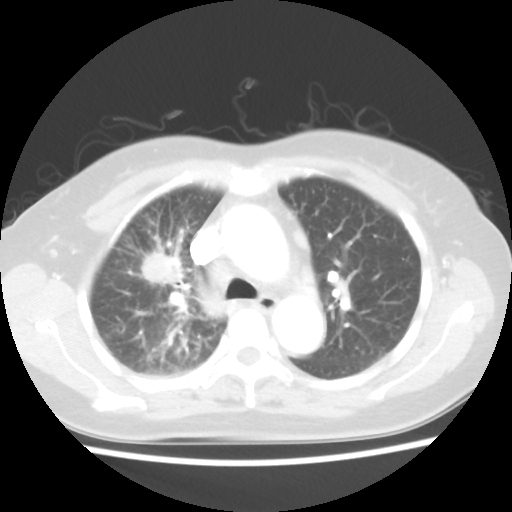
Chest CT, one axial slice; slice 31 of 48 in the series (ordered by position); 100 kVp; lung window (W 1500 / L -600 HU); 512 × 512 image matrix, field of view 312 × 312 mm. Patient: female, 55 years. Case-level facts recorded for this patient, not image findings: clinical TNM (as recorded): T1b N3 M1a.
Outlined on this slice (bounding box drawn by a radiologist):
- lung tumour (recorded histology: adenocarcinoma): box from (x=142, y=253) to (x=183, y=283) px